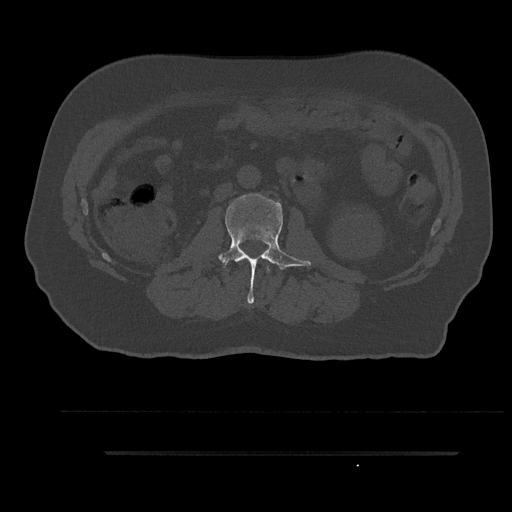
CT including the spine, one axial slice; position 108 of 797 along the scan axis; reconstruction kernel Br40s/3; 120 kVp; bone window (W 1800 / L 400 HU); 0.5 mm slice thickness; 512 × 512 image matrix. Patient: male, 63 years. Case-level facts recorded for this patient, not image findings: primary cancer: renal; vertebrae with lytic lesions (as recorded): T8.
Outlined on this slice (semi-automatically segmented with operator editing):
- L1 vertebra: bounding box <266,267,269,272> (left, top, right, bottom; pixels)
- L2 vertebra: <218,194,311,304>